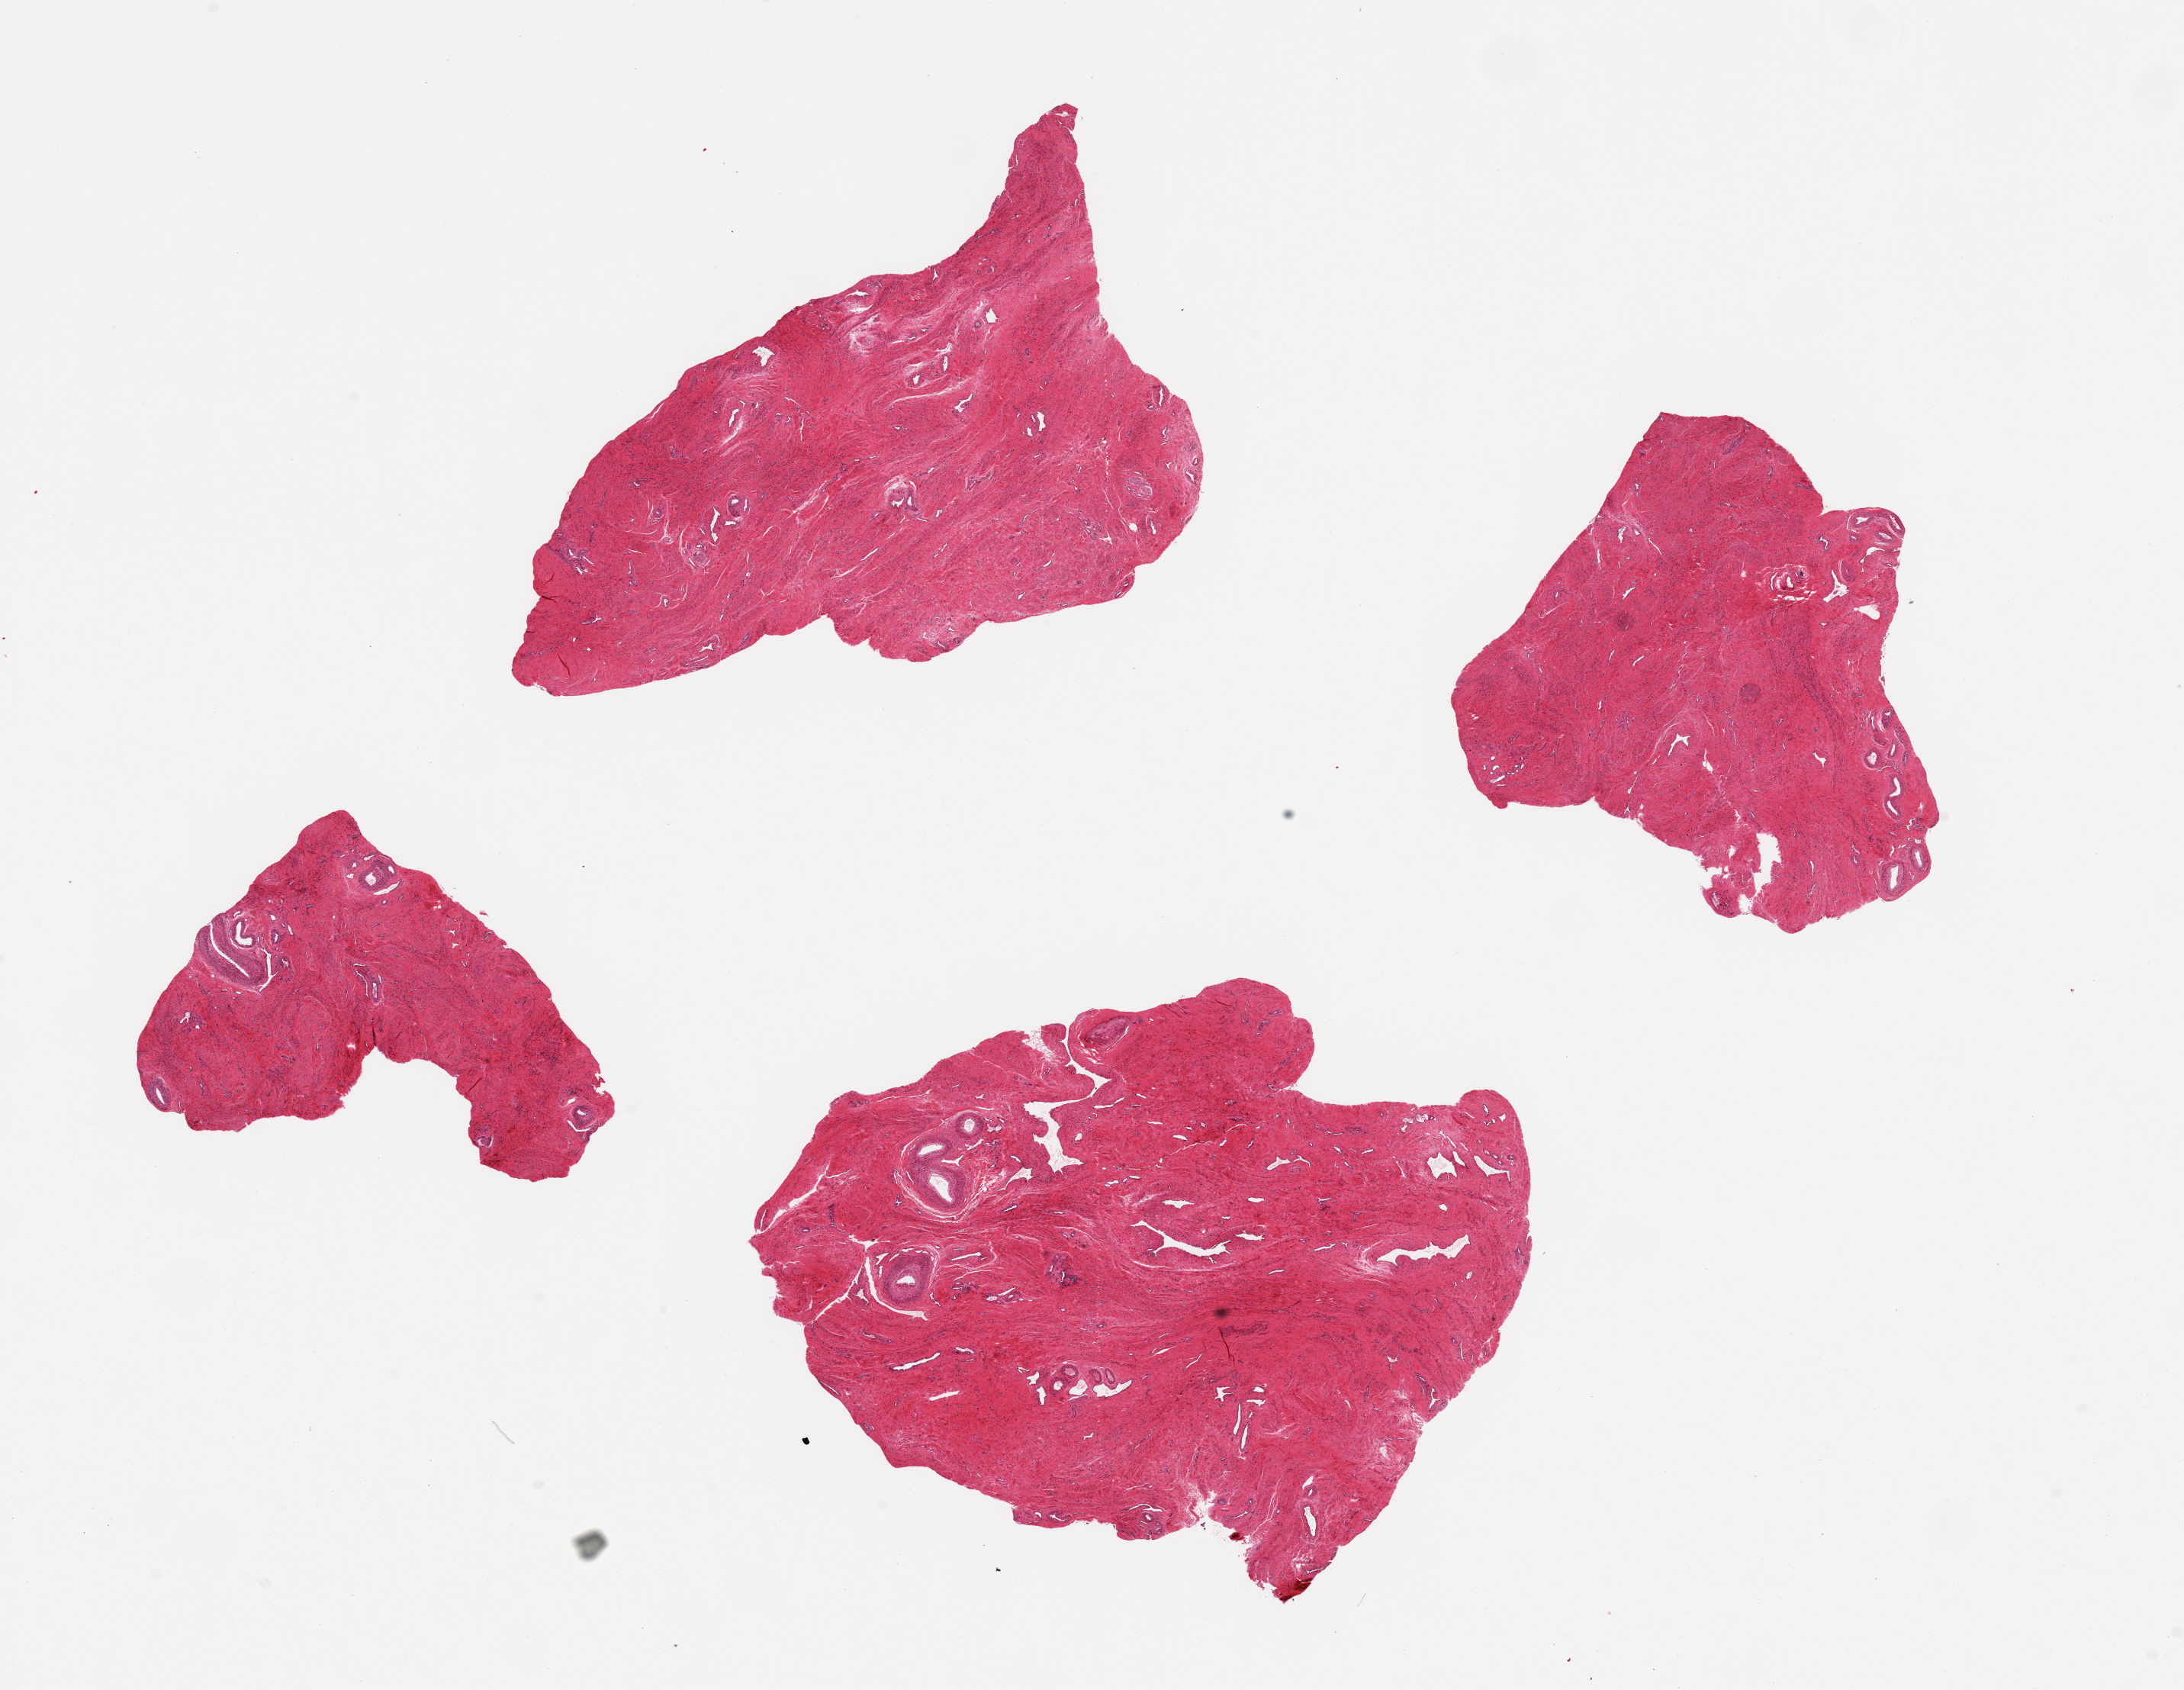
Digitized haematoxylin and eosin-stained section — a low-resolution overview of the entire scanned area, about 22.6 x 17.5 mm; PAXgene-fixed, paraffin-embedded tissue; sampled site (target tissue): endocervix; donor tissue sample. Donor sex: female.
Reviewer comment on this tissue sample: 4 aliquots, ~7x4mm. All stroma, no endocervical glands noted.